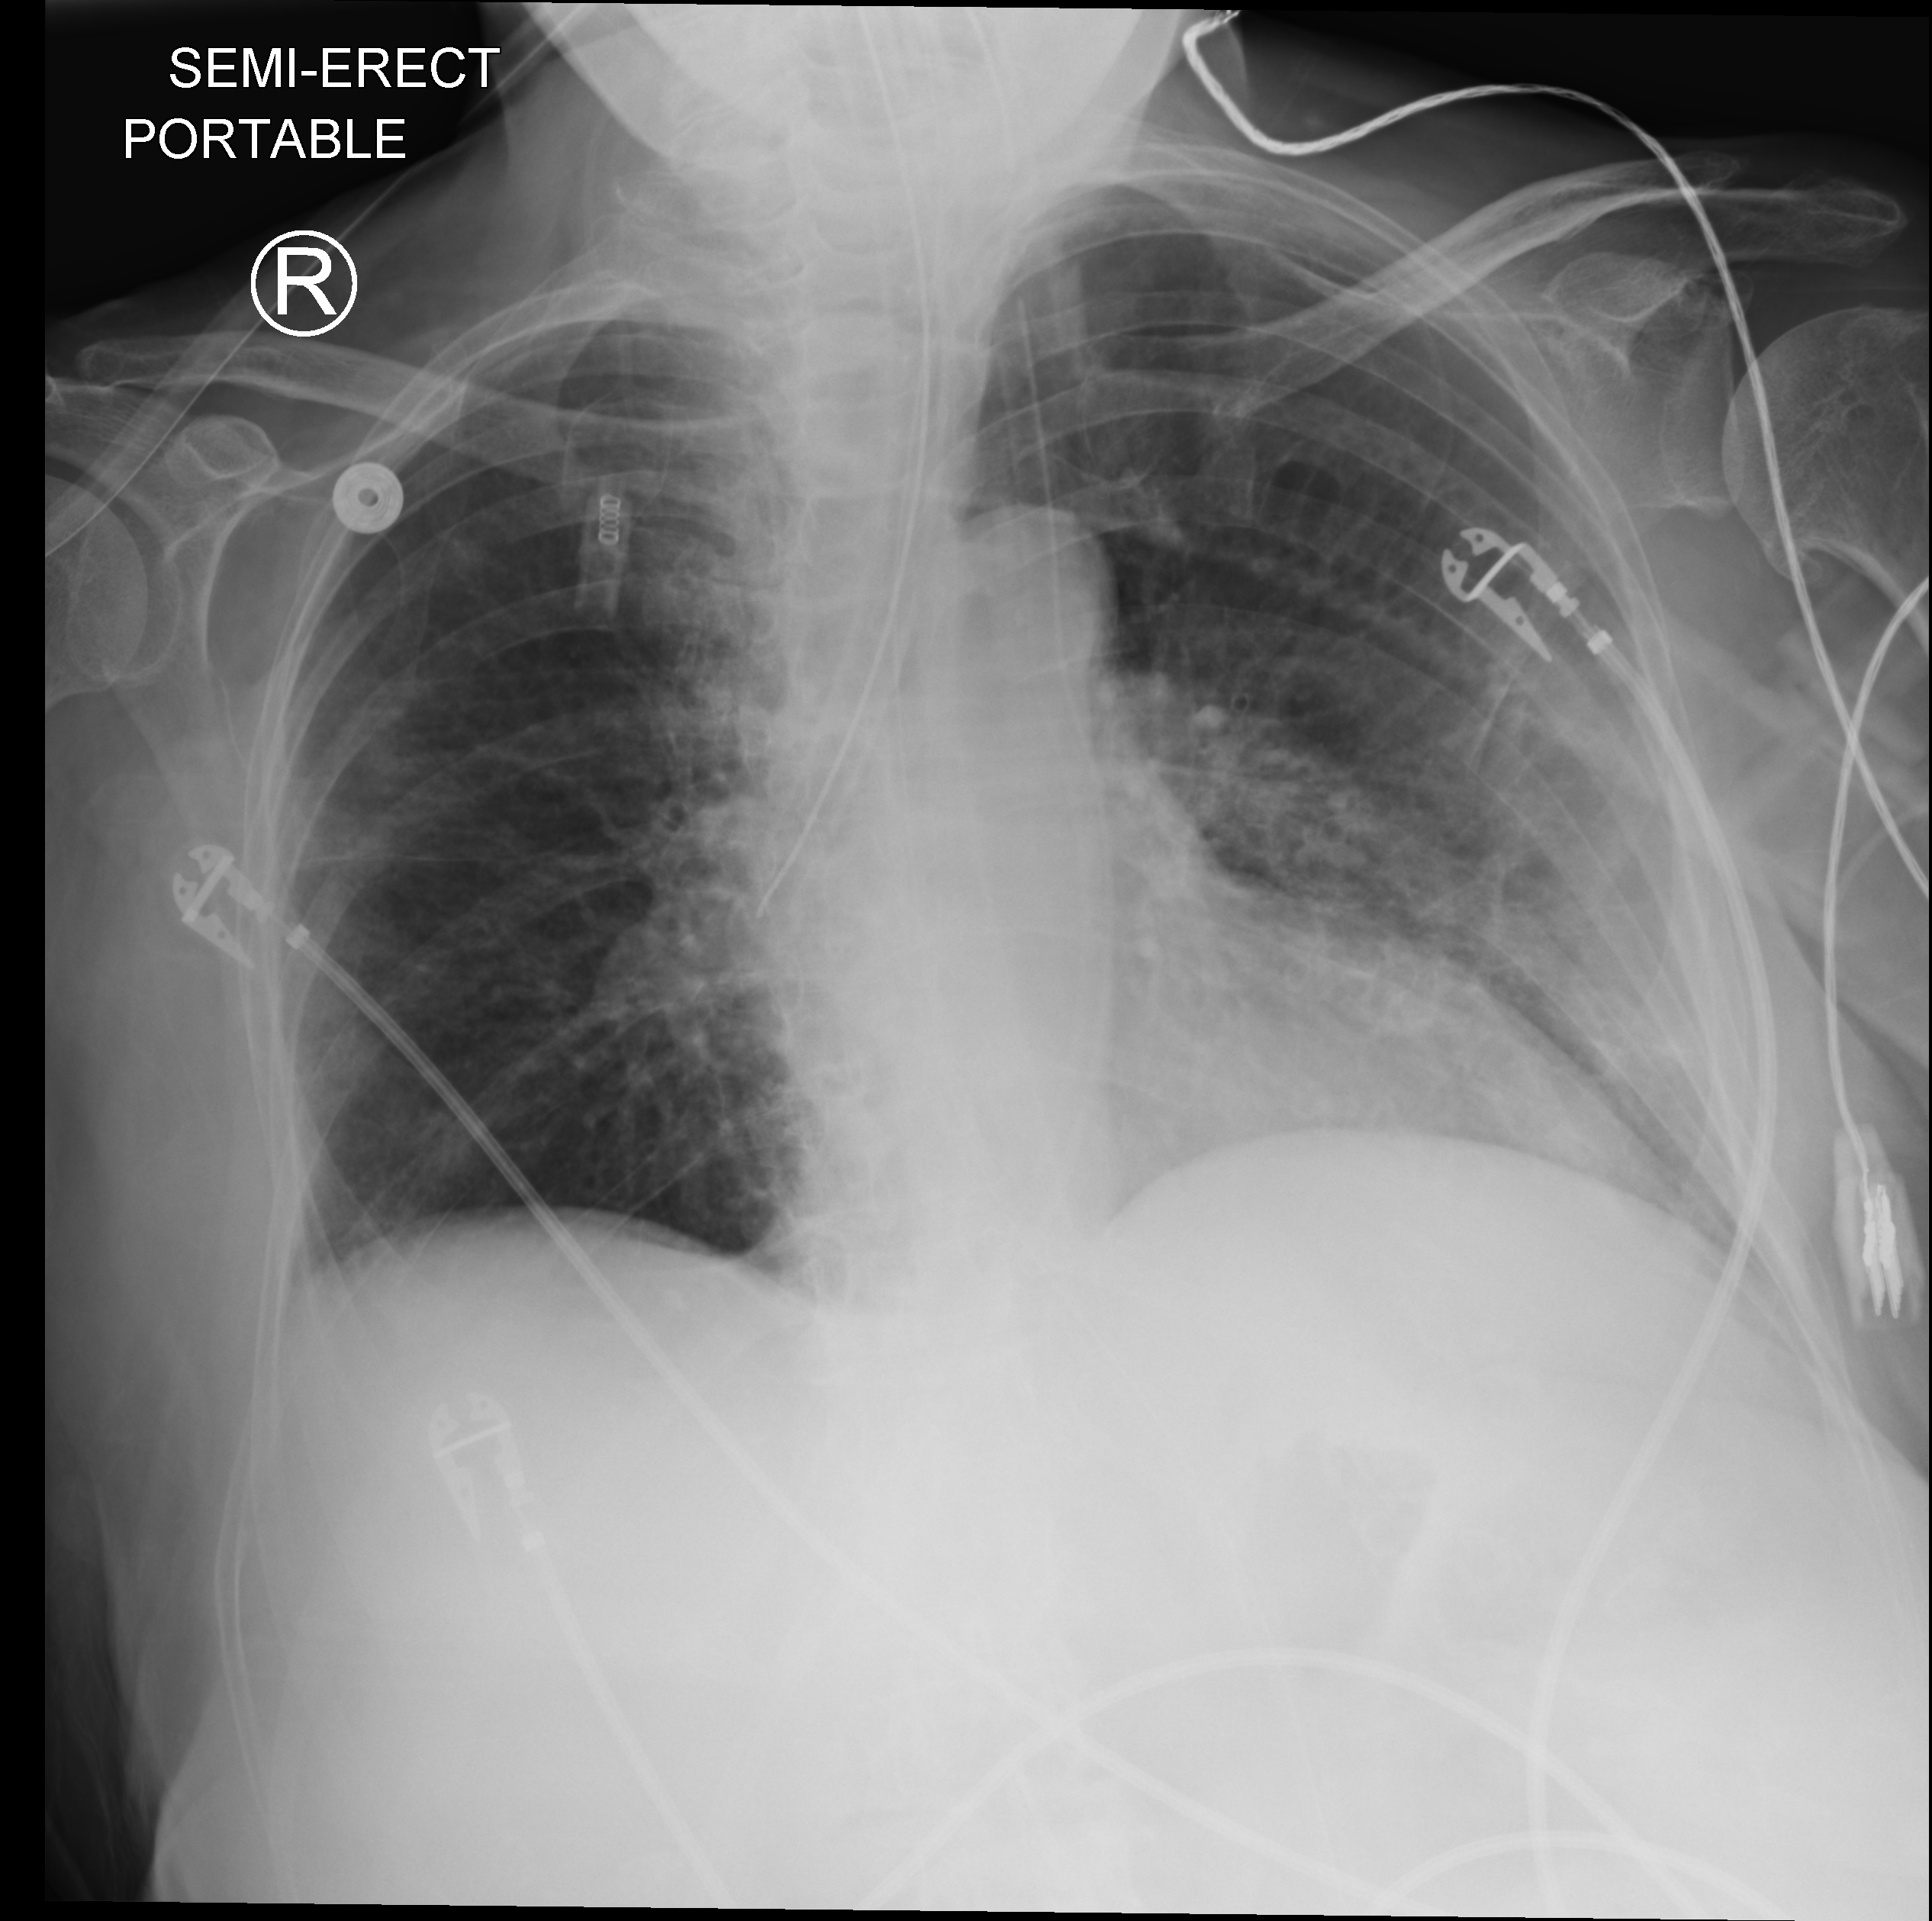
Portable chest radiograph, anteroposterior (AP) projection. Patient hospitalised with COVID-19; female, aged 75–90 years.
Admission-level facts for this patient (not findings on this image; timing relative to this image not recorded): admitted to intensive care during this hospital stay: yes; mechanically ventilated during this hospital stay: yes; length of hospital stay: 82 days.